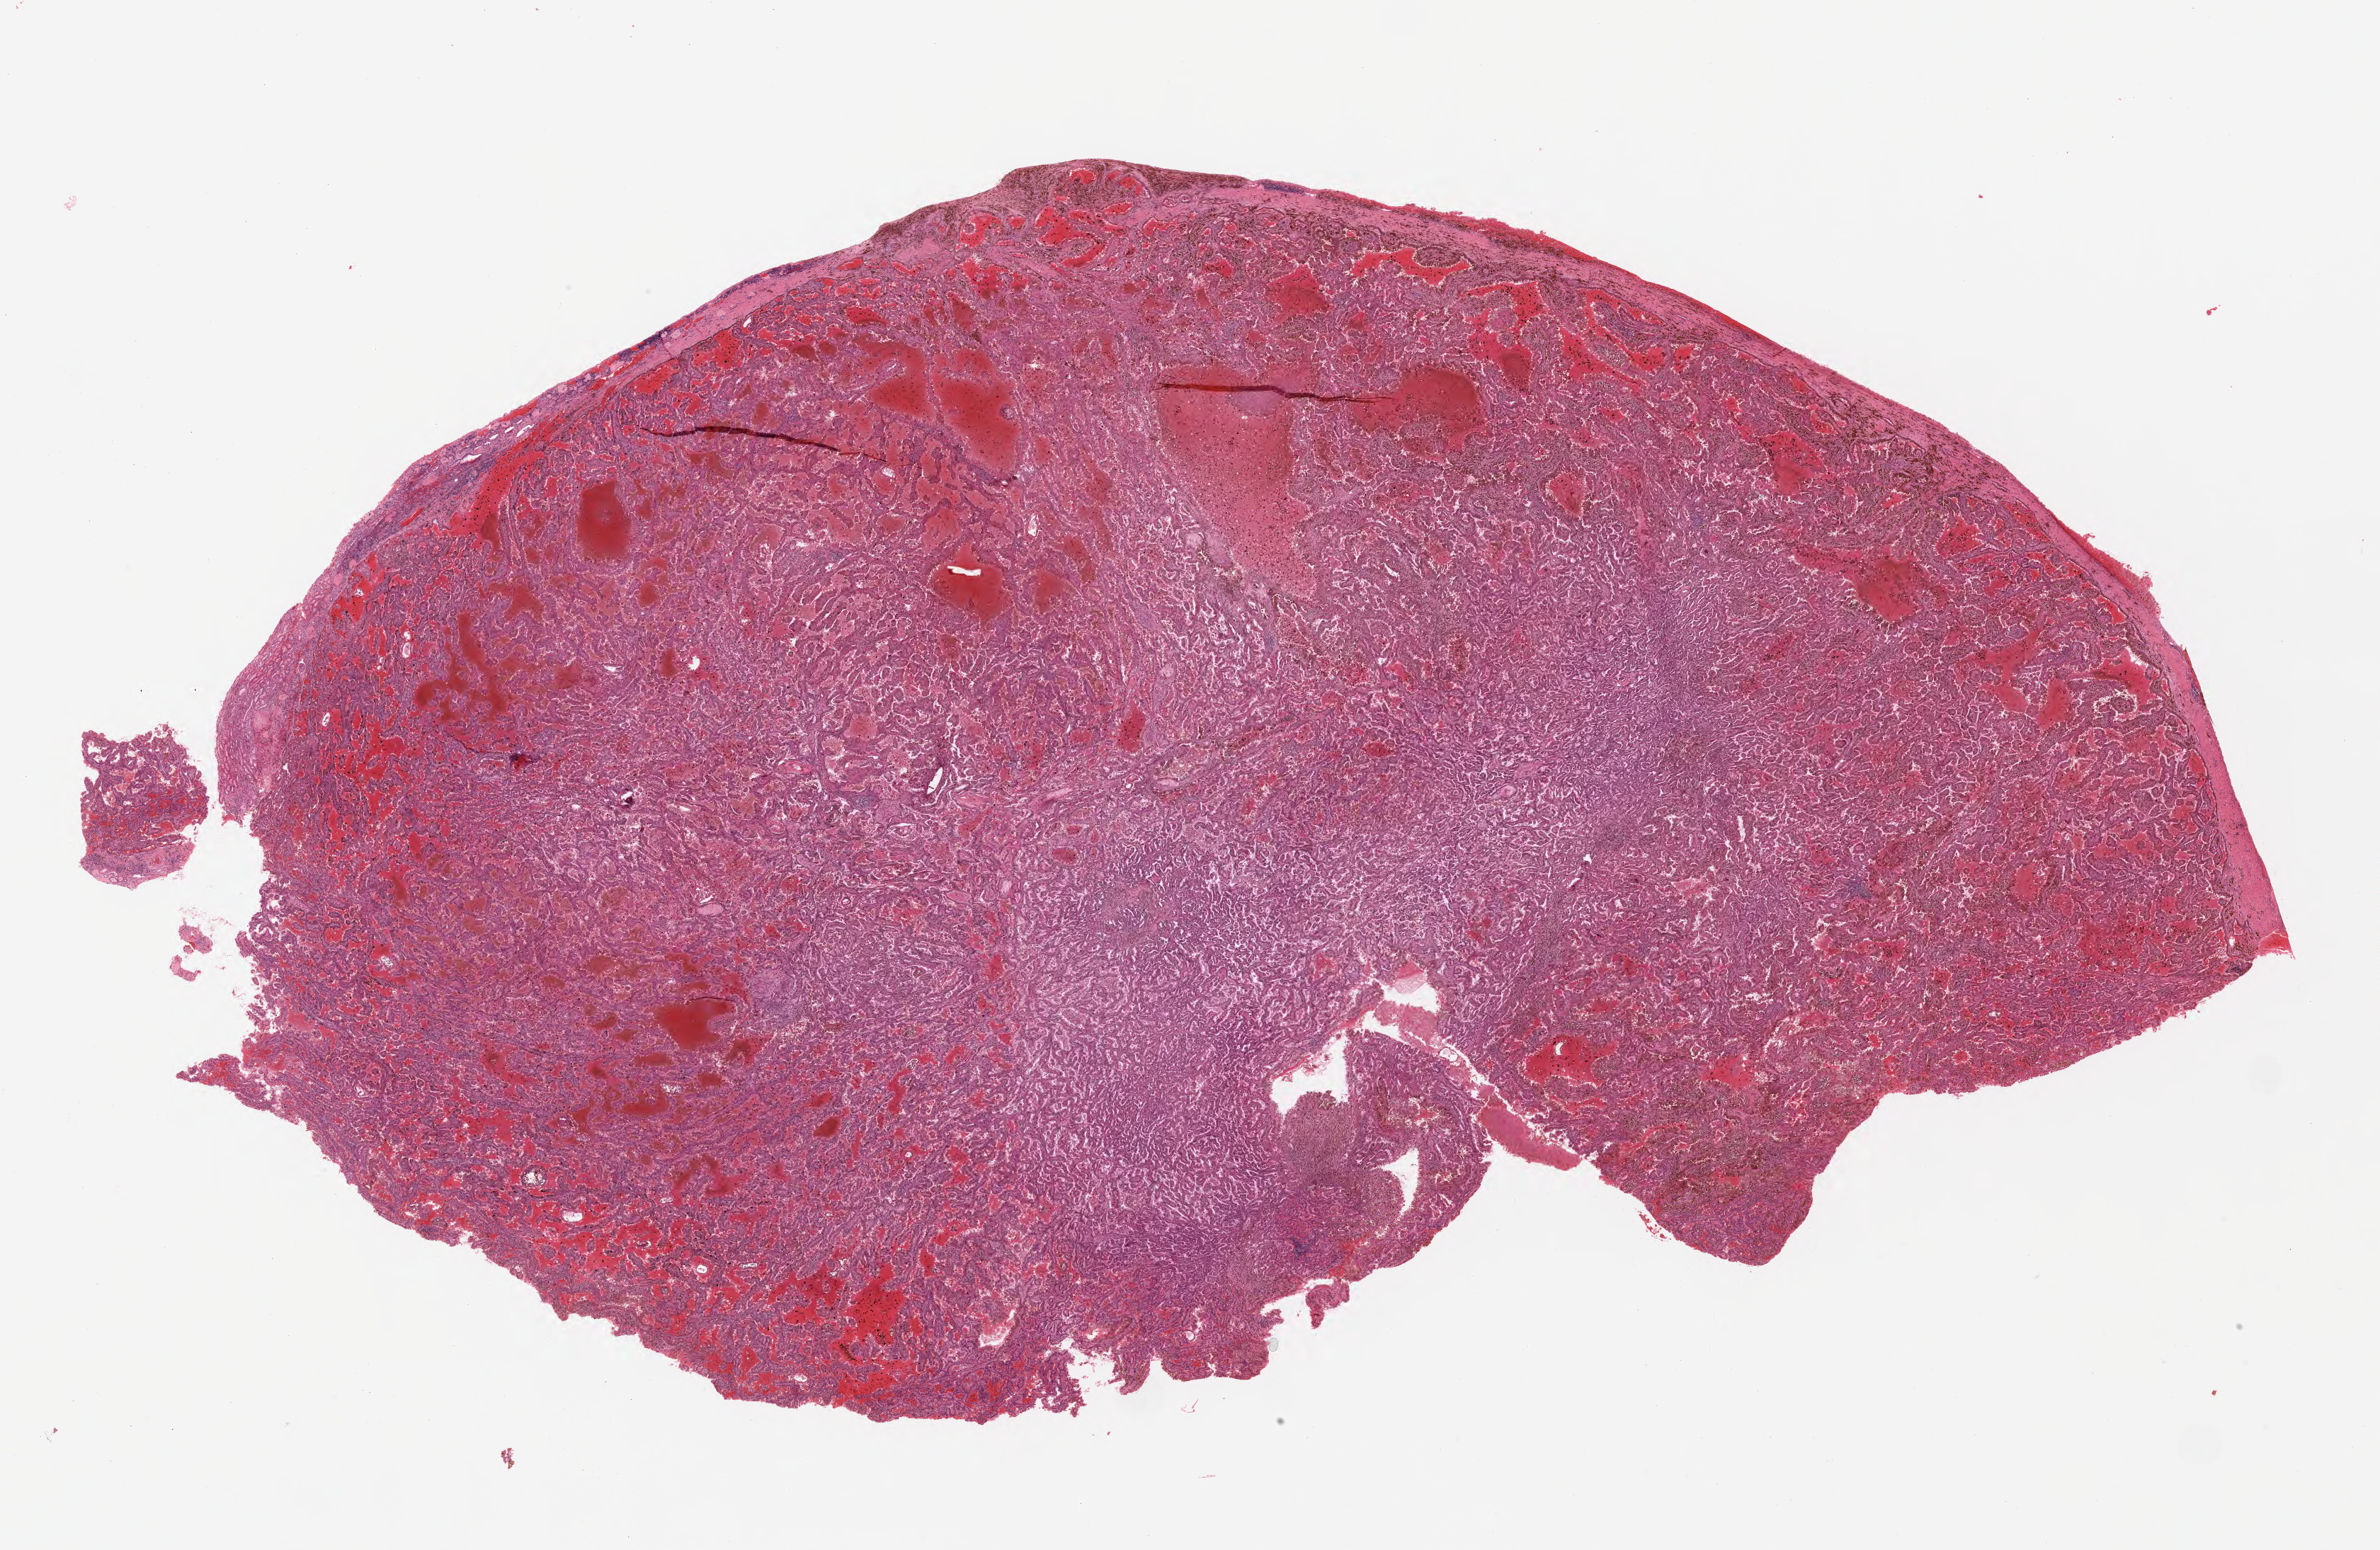
Whole-slide histology image, Hematoxylin and eosin (H&E) stained, a low-resolution overview of the entire scanned area, about 26.5 x 17.3 mm (from a 20x scan), formalin-fixed paraffin-embedded (FFPE) diagnostic section, primary tumour sample from the kidney. Patient: male, age at initial diagnosis 81 years.
• pathologic diagnosis: Papillary adenocarcinoma, NOS